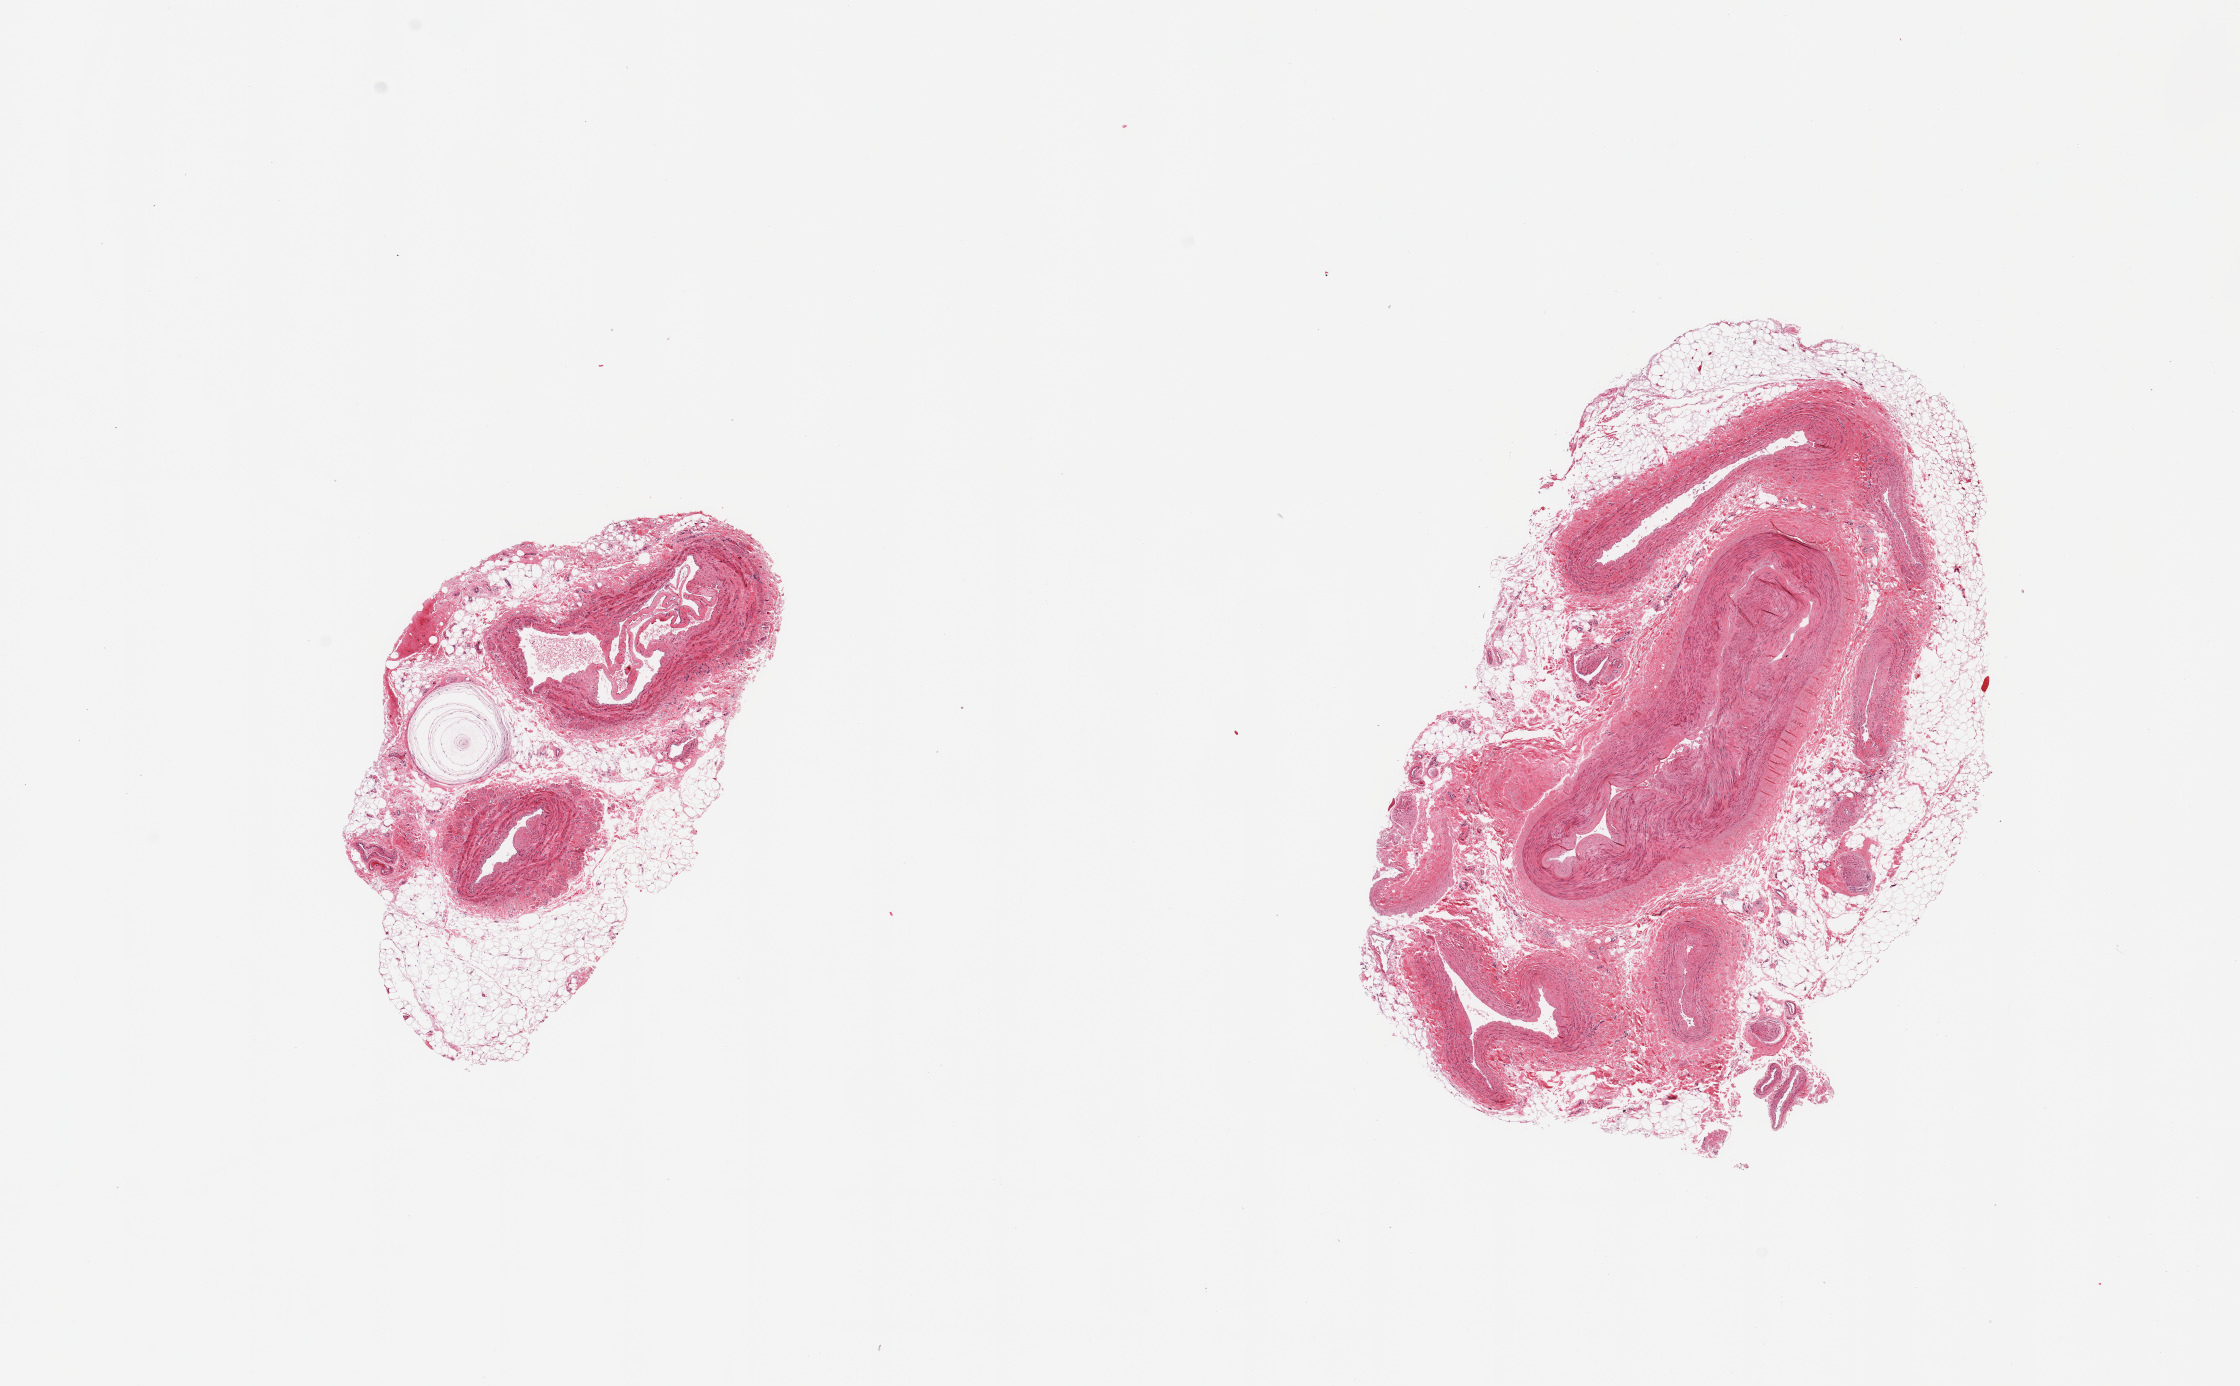
Hematoxylin and eosin (H&E) whole-slide image, brightfield, whole scanned area (about 17.7 x 11.0 mm, acquisition: 20x scan) shown as a low-resolution overview. Donor sex: male.
Specimen: PAXgene-fixed paraffin-embedded (PFPE) section; sampled site (target tissue): tibial artery; donor tissue sample.